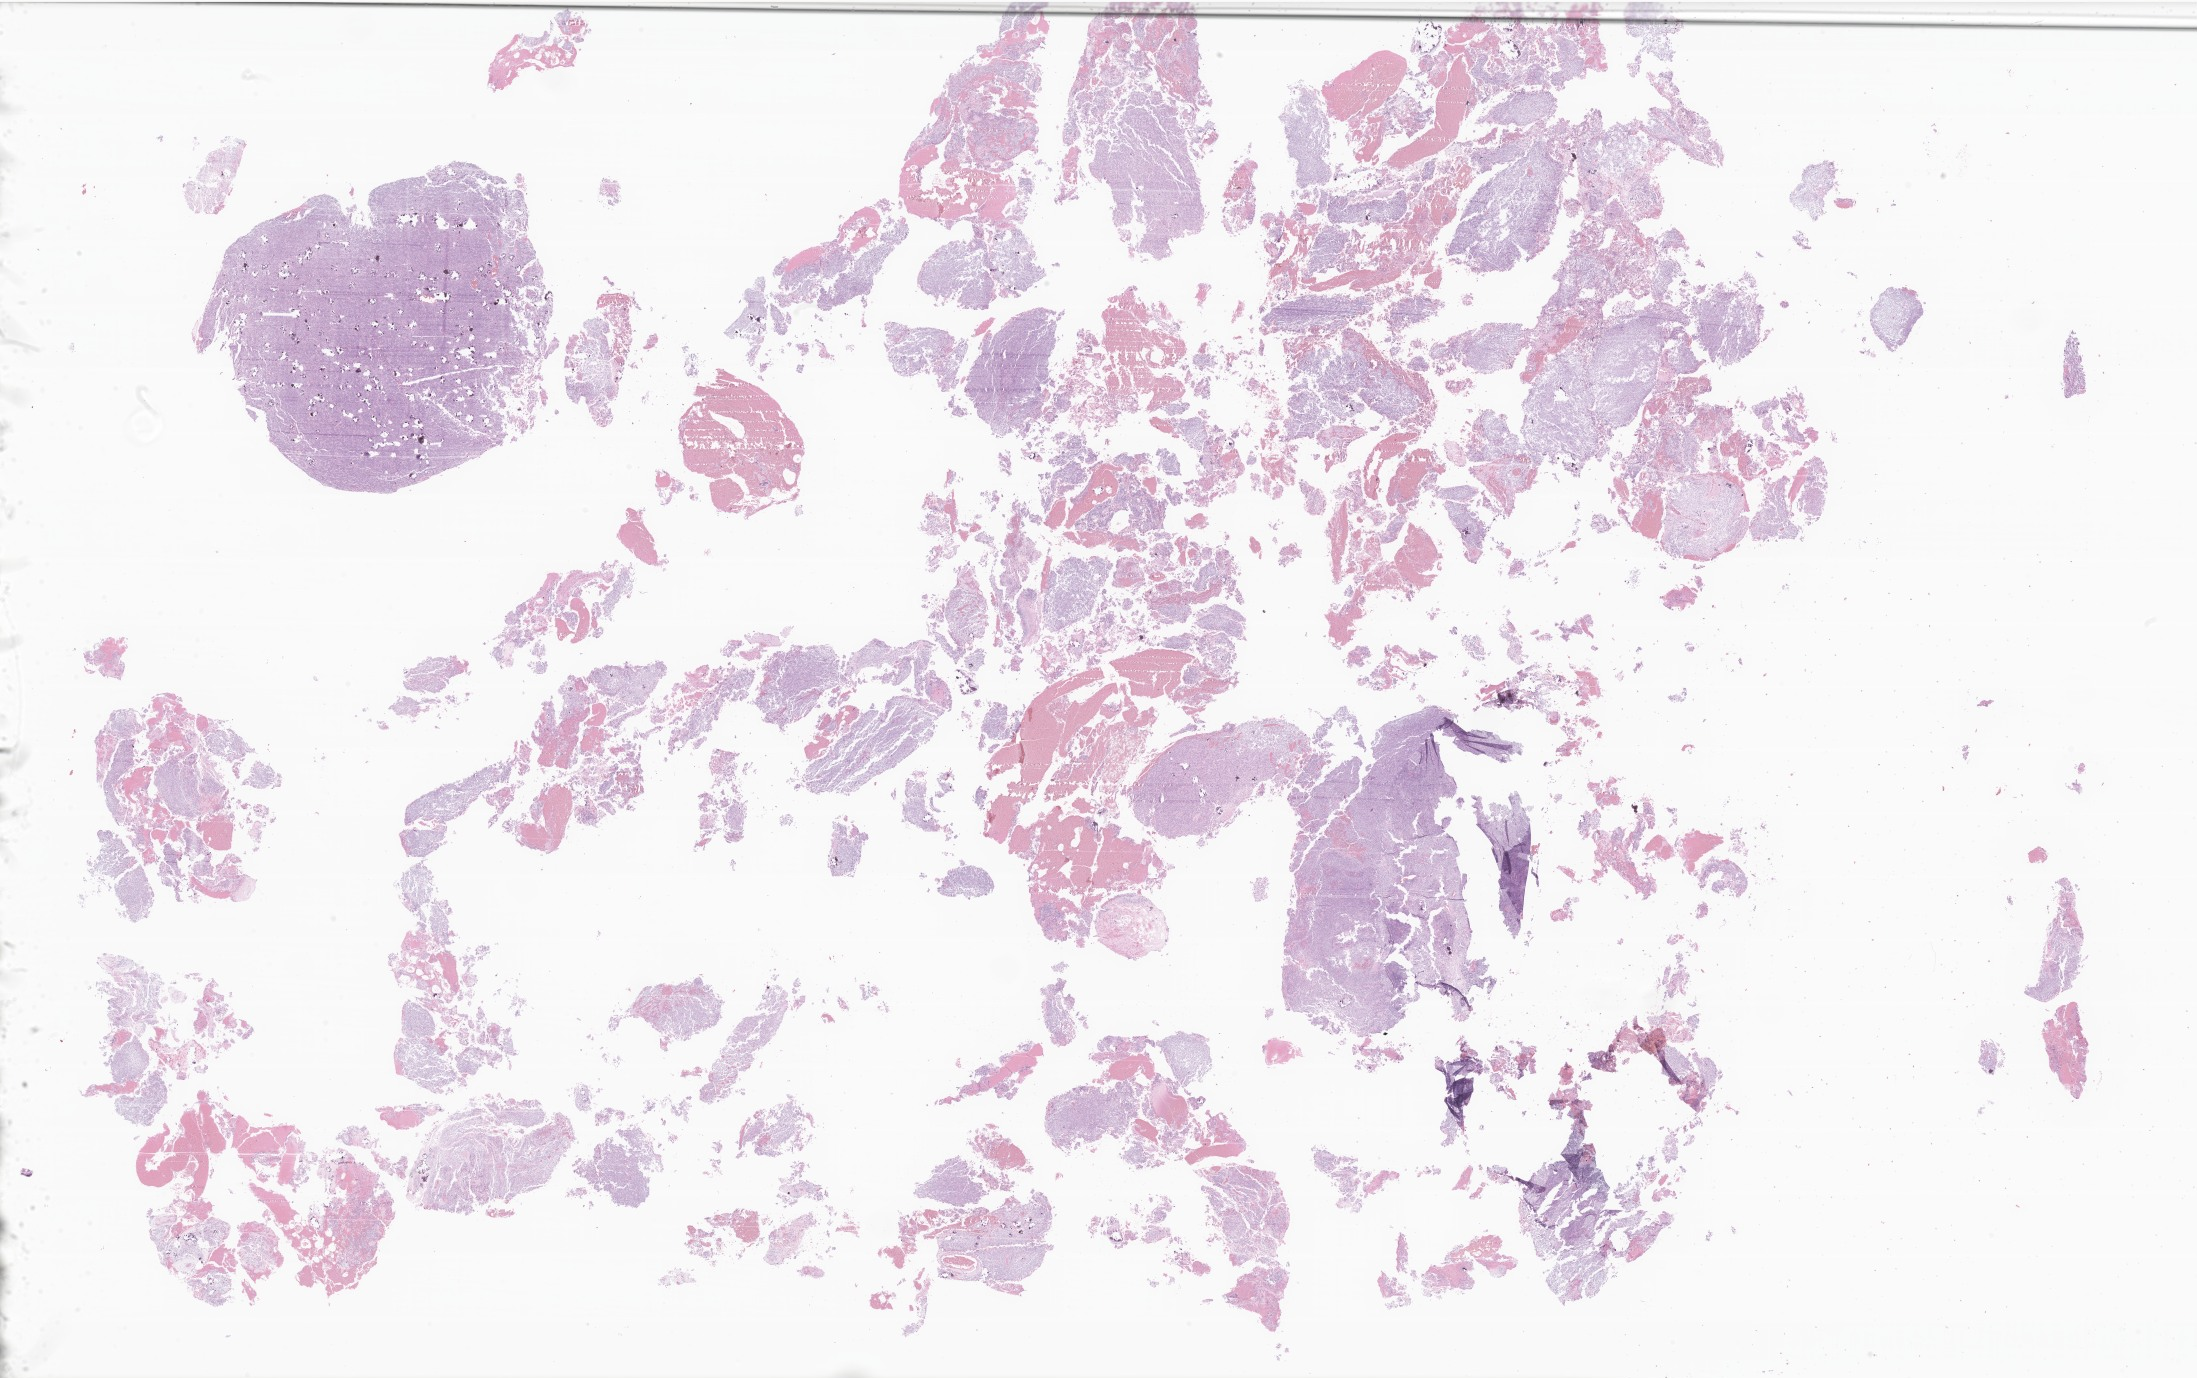
Whole-slide image, hematoxylin and eosin (H&E) stain of tumor tissue from the brain — shown as a low-resolution overview of the whole scanned area (about 37.0 x 23.2 mm). Formalin-fixed, paraffin-embedded (FFPE) tissue. Patient female; age 178 months (14 years 10 months).
Recorded diagnosis: Central neurocytoma.